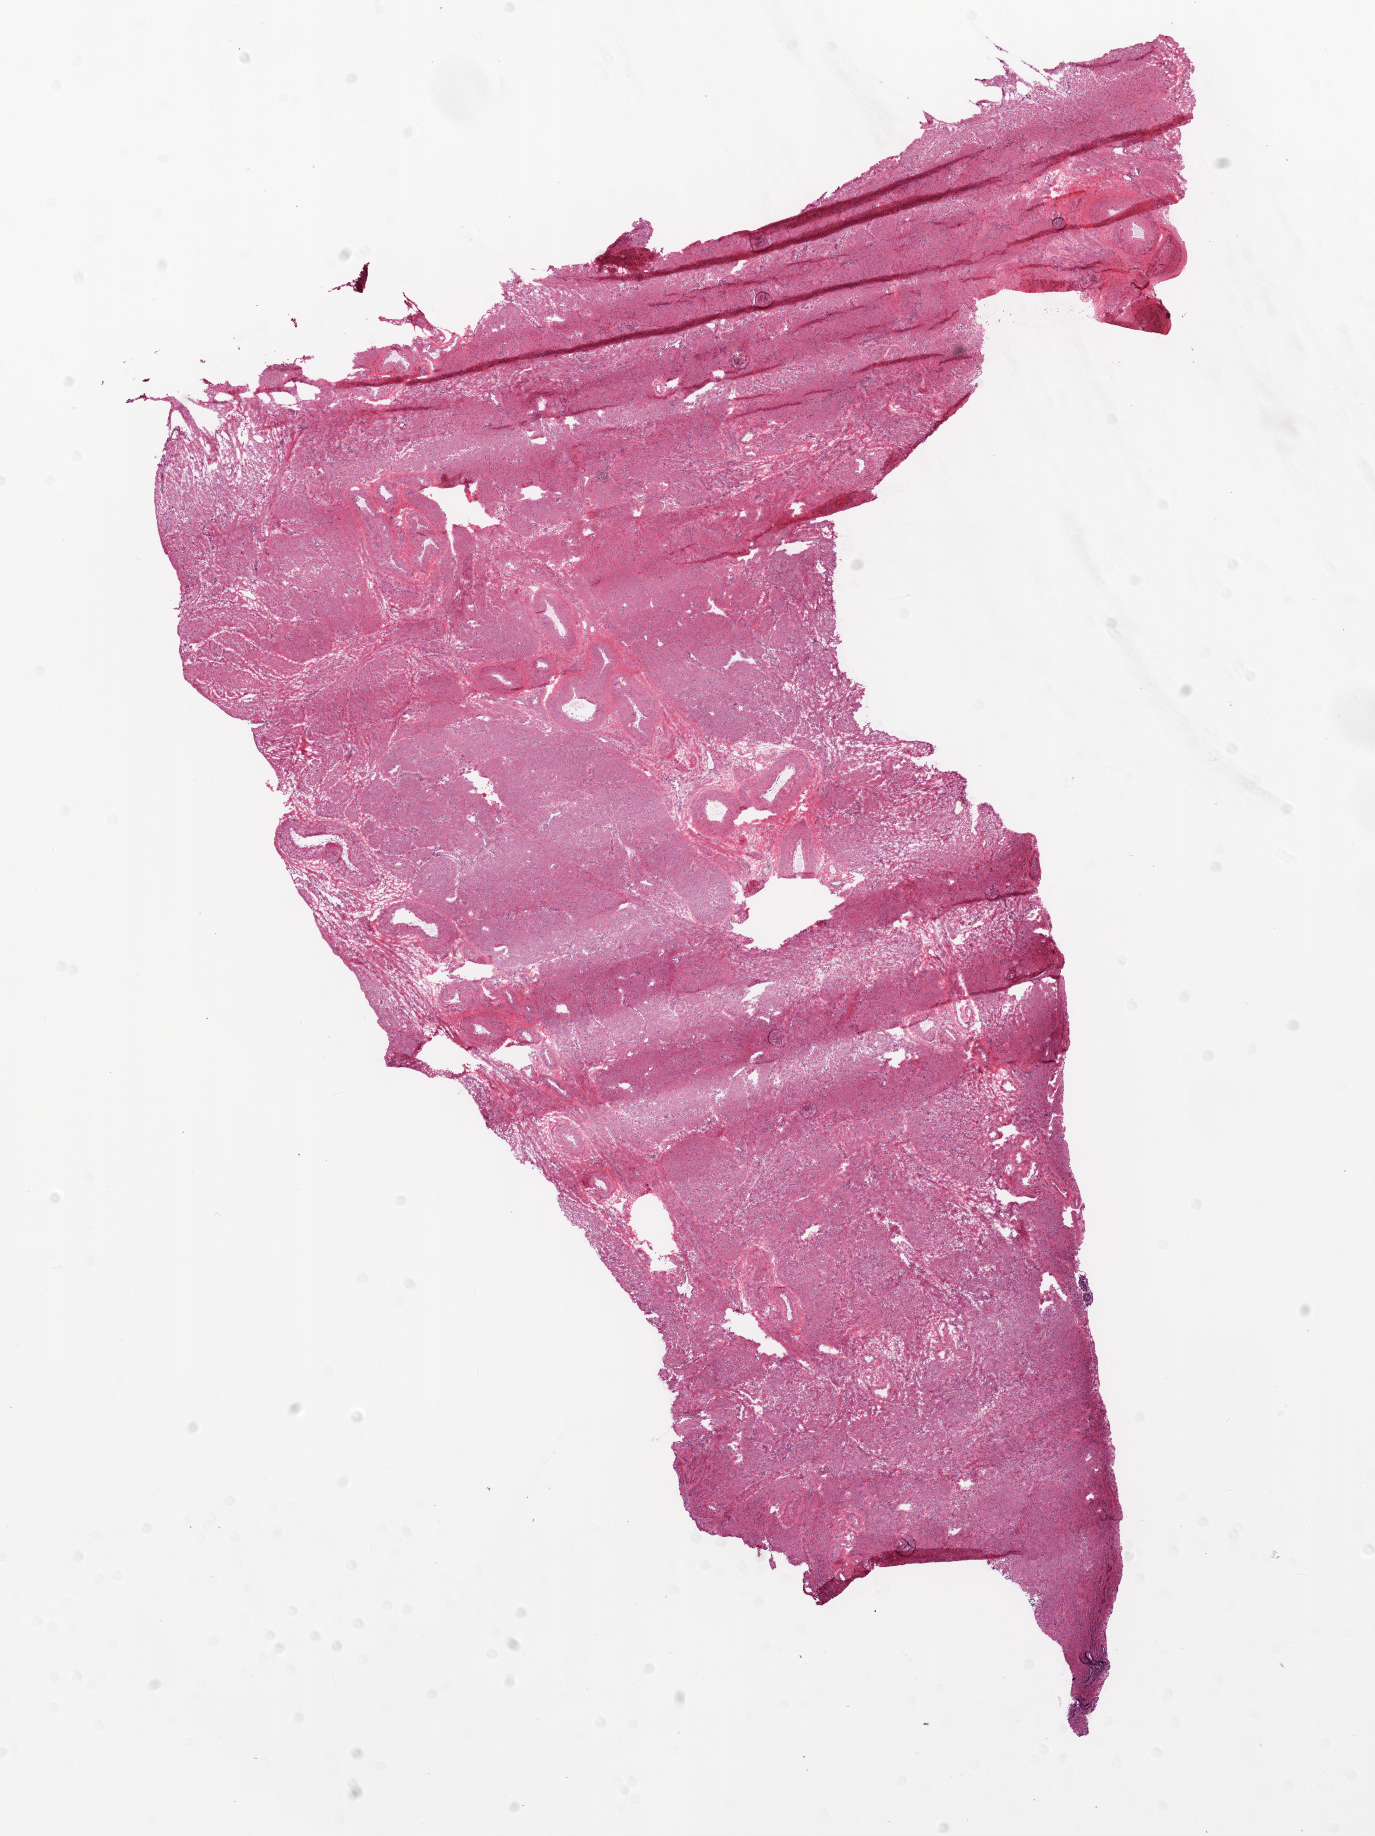
H&E whole-slide image, a low-resolution overview of the entire scanned area, about 11.0 x 14.7 mm (acquisition: 20x scan); frozen section; ovary, solid tissue normal (non-tumour tissue) sample. Patient: female, age at initial diagnosis 37 years.
This section: solid tissue normal sample (biorepository sample class). Patient diagnosis: Serous cystadenocarcinoma, NOS.